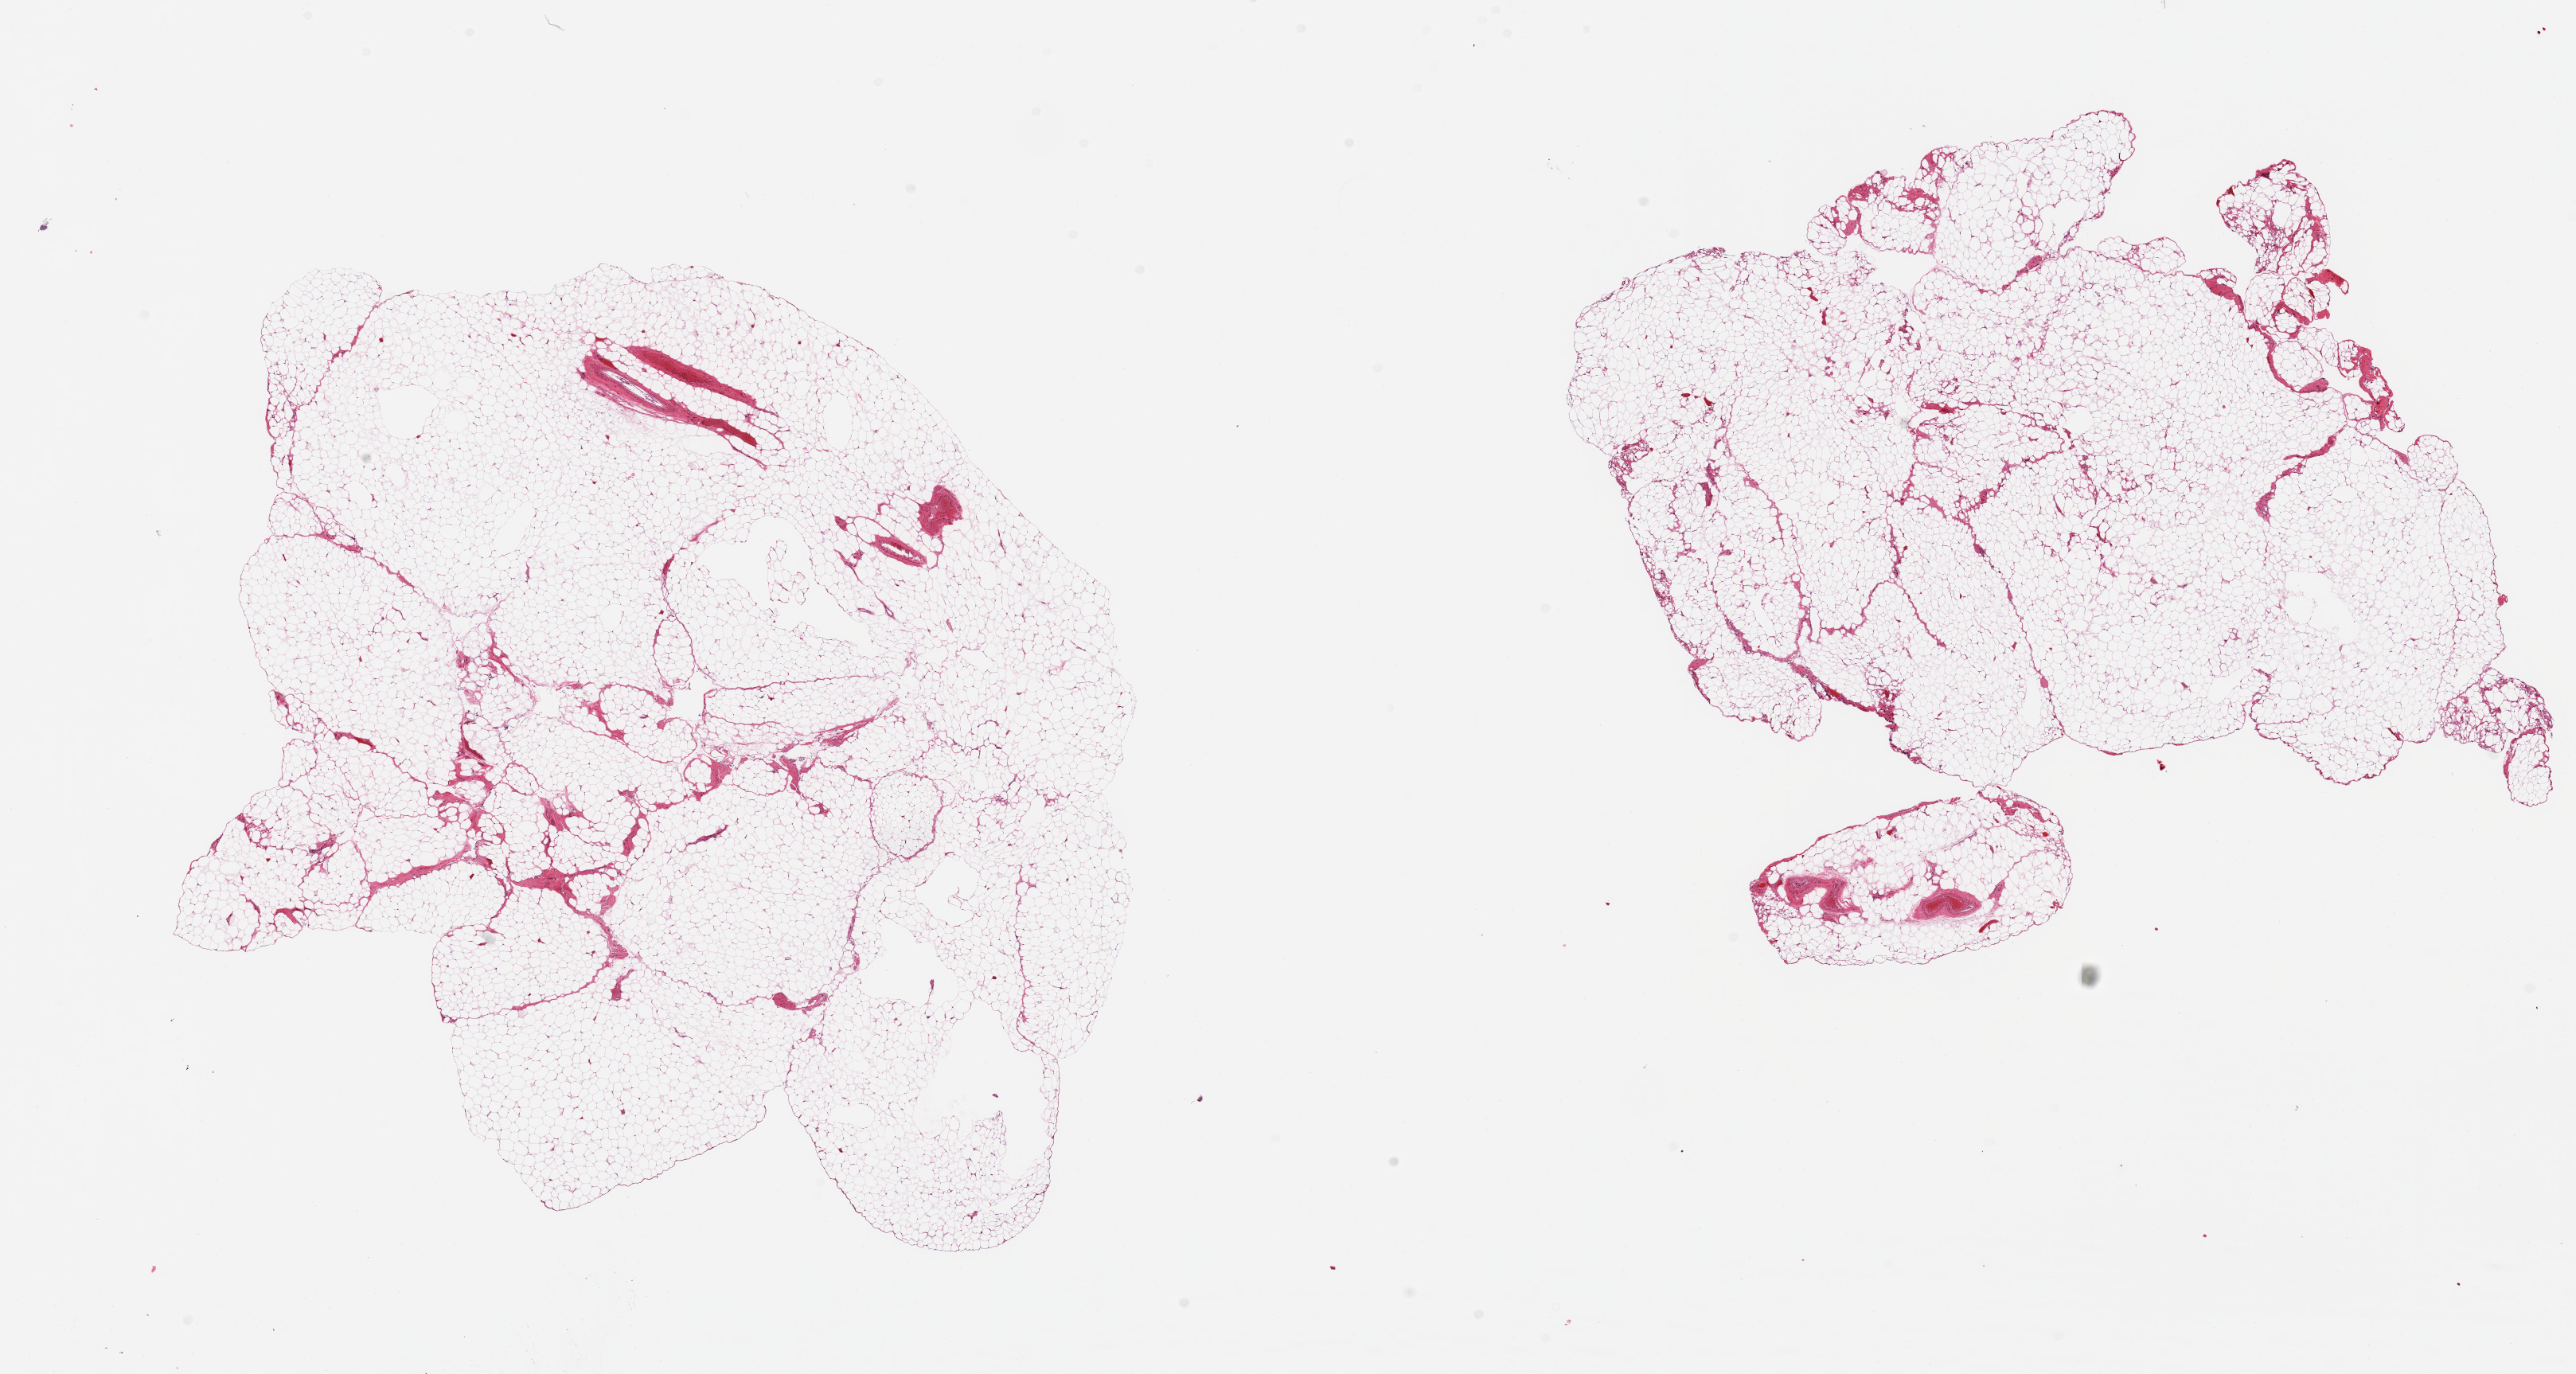
Digitized hematoxylin and eosin (H&E)-stained section, brightfield, low-resolution overview of the scanned area, about 25.6 x 13.7 mm. PAXgene-fixed paraffin-embedded (PFPE) section. Section of omentum (target tissue). Donor tissue sample.
Reviewer comment on this tissue sample: 2 pieces, ~5-10% vascular elements.